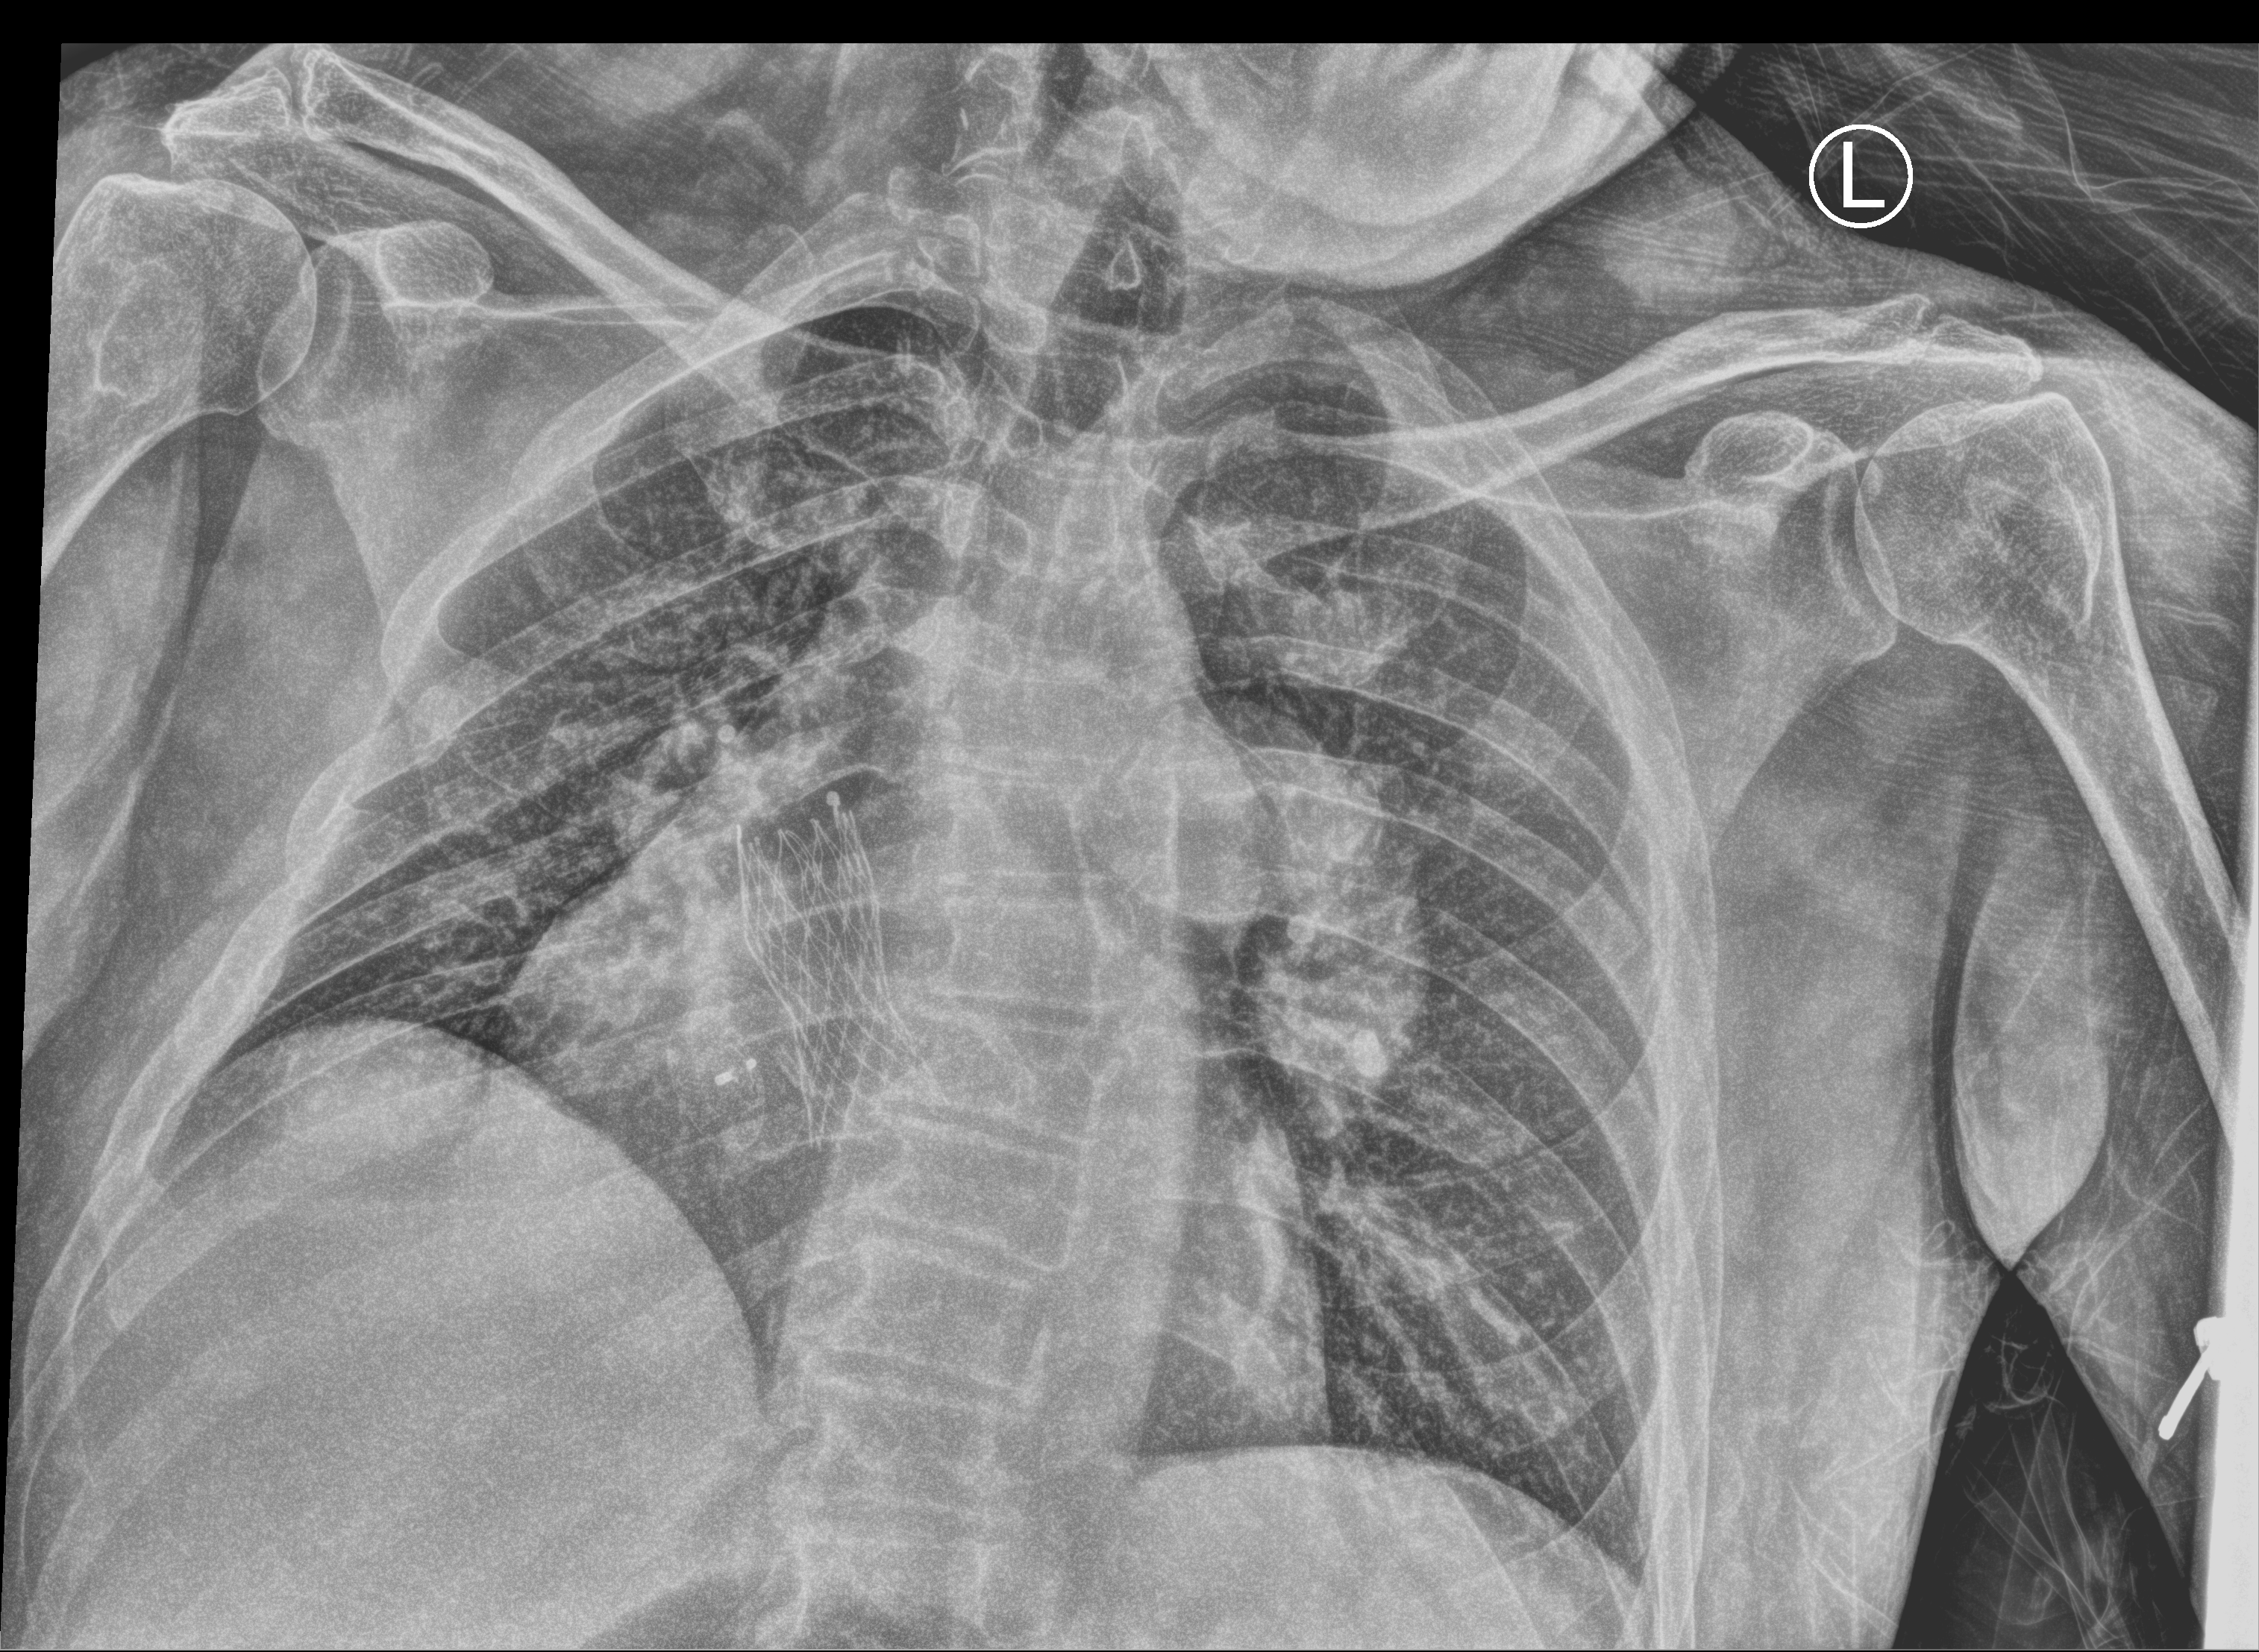
Bedside chest radiograph (computed radiography), anteroposterior (AP) projection. Male patient hospitalised with COVID-19, age 60–74 years.
Hospital-stay facts (about this admission, not read from this image; timing relative to this image not recorded):
- mechanically ventilated during this hospital stay: no
- admitted to intensive care during this hospital stay: no
- length of hospital stay: 6 days